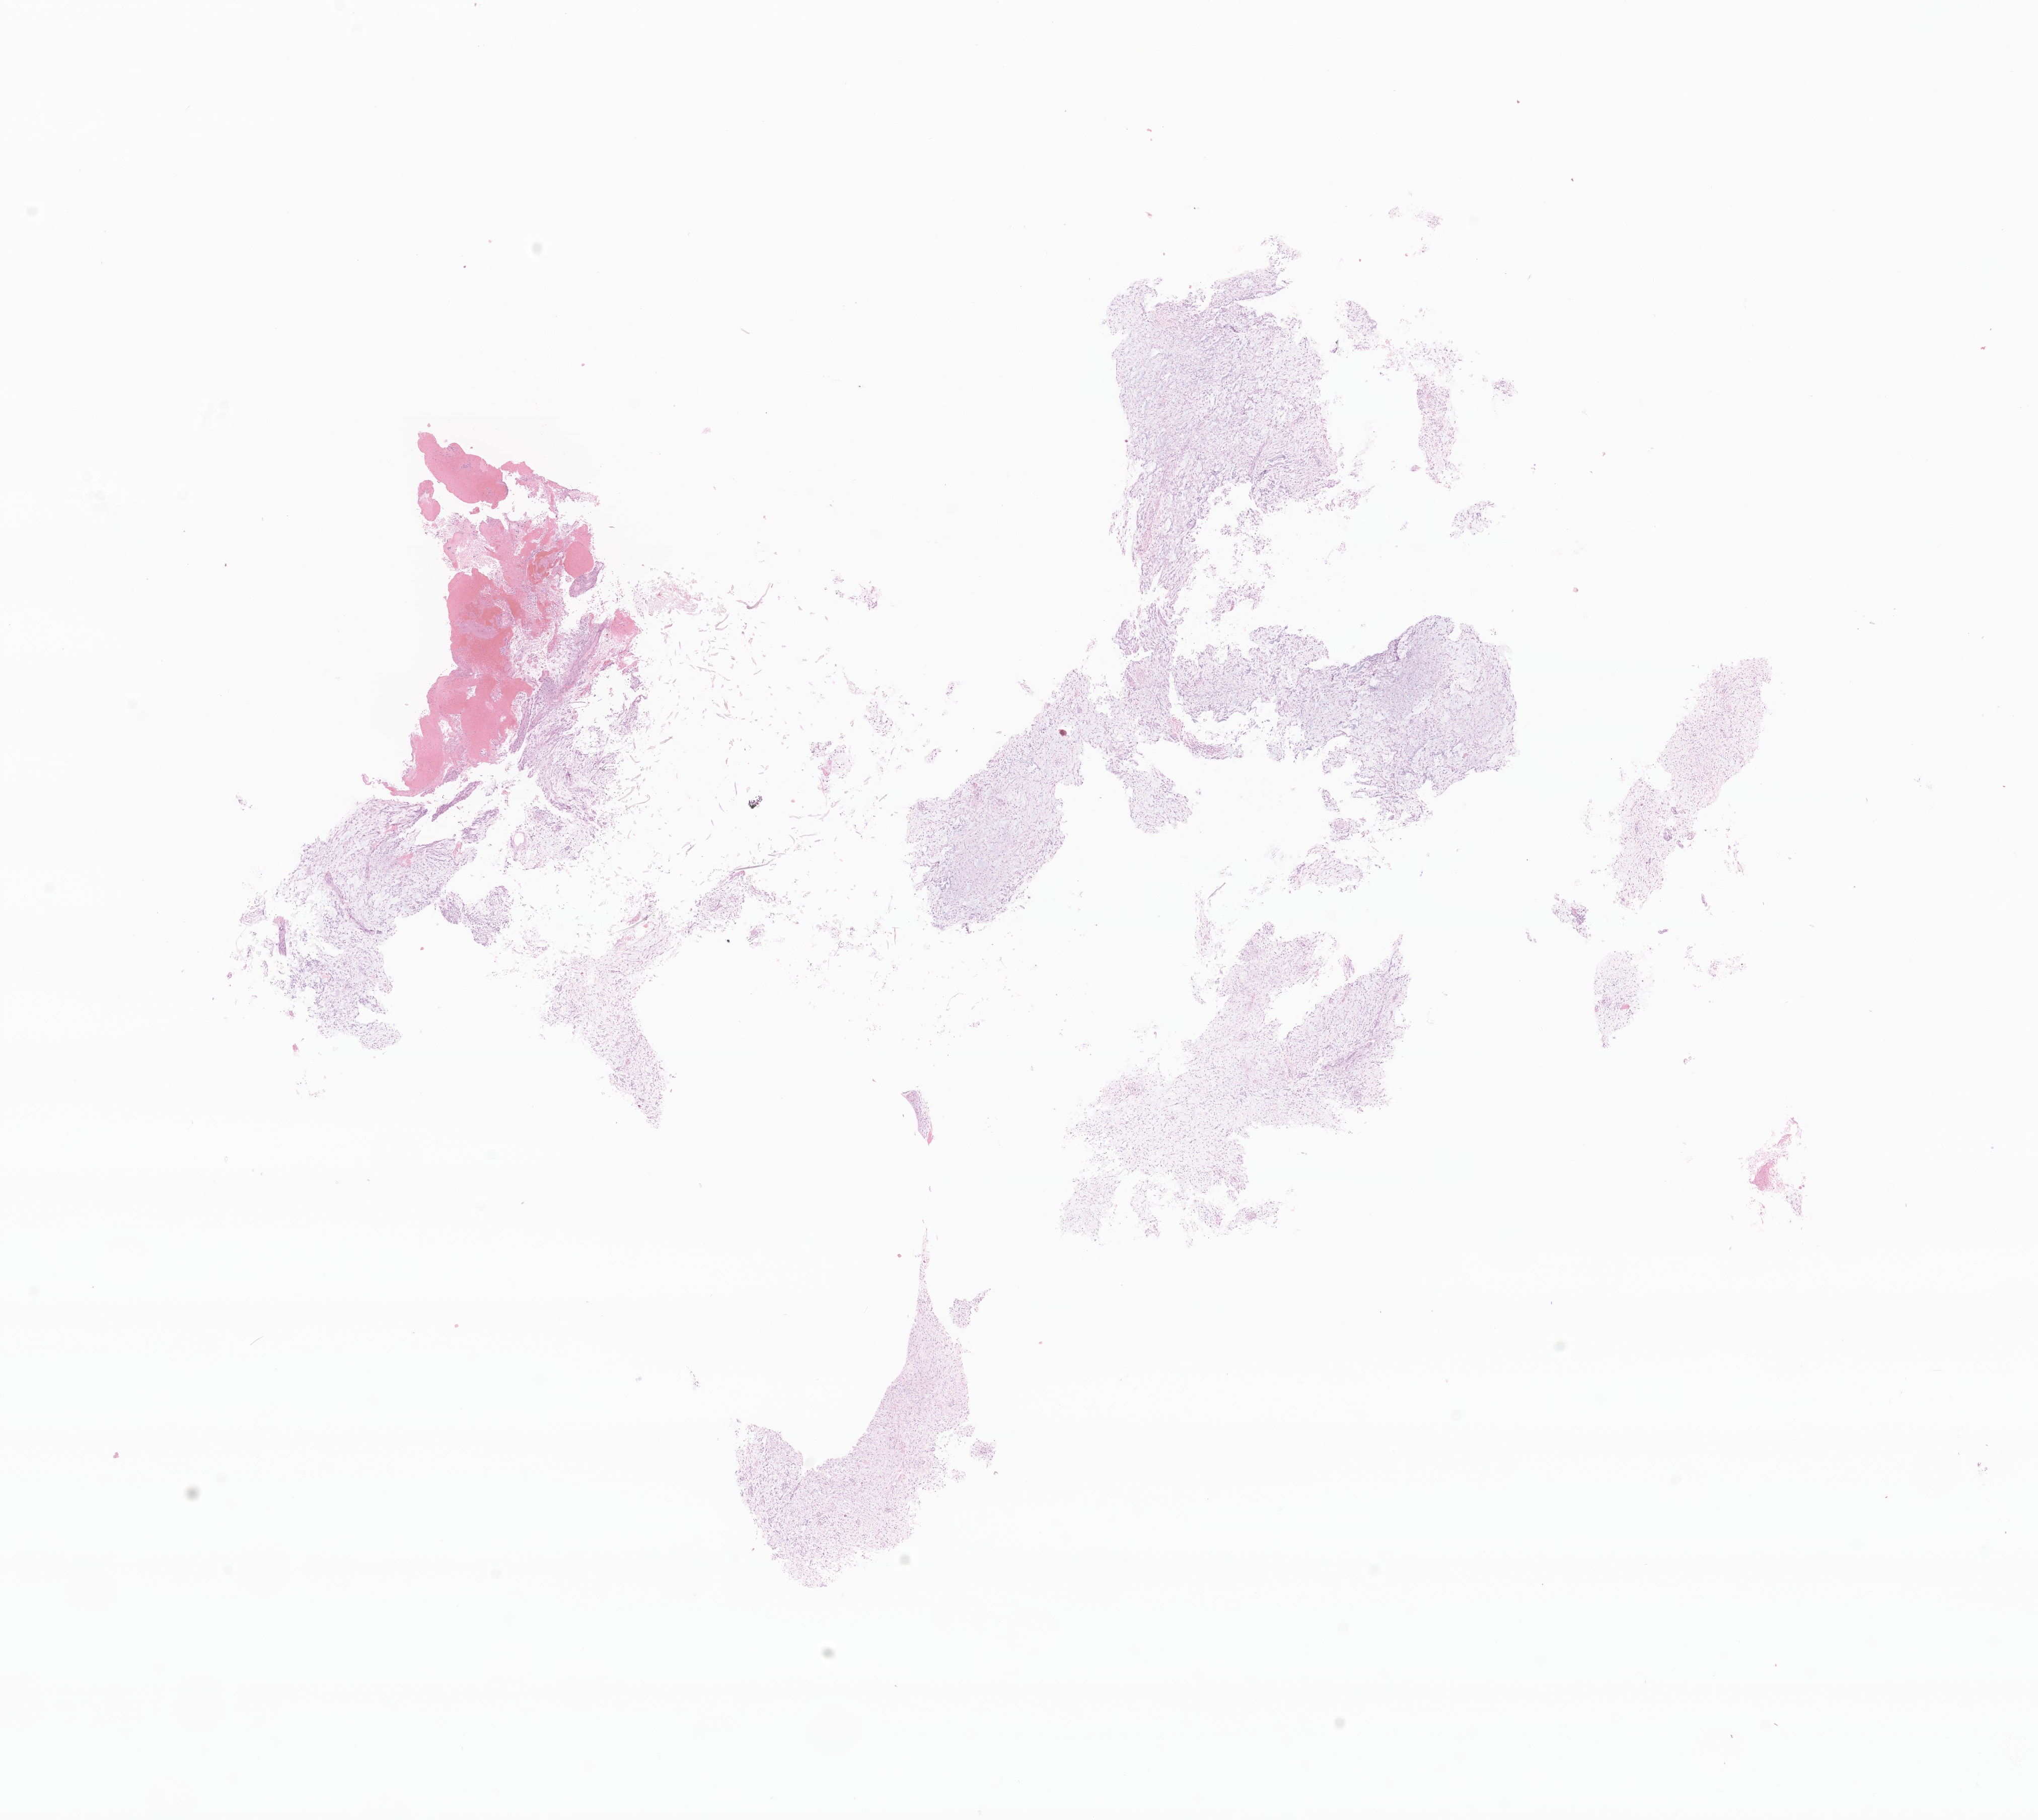
Whole-slide image, haematoxylin and eosin stain of tumor tissue from the brain — low-resolution overview of the scanned area, about 17.1 x 15.2 mm, formalin-fixed, paraffin-embedded (FFPE) tissue. Female patient, age 84 months (7 years).
Diagnosis: Pilocytic astrocytoma.